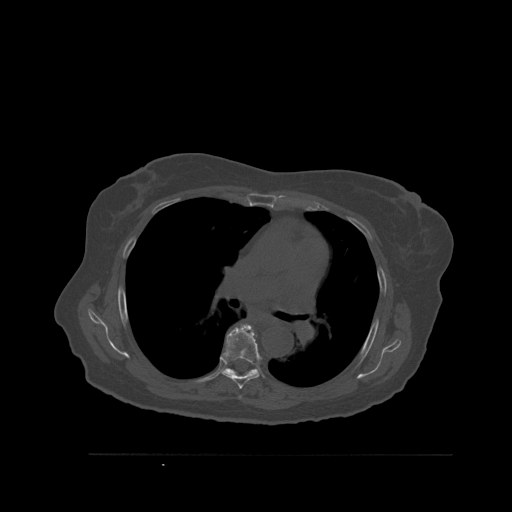
CT including the spine, one axial slice; bone window (W 1800 / L 400 HU); 1.5 mm slice thickness; 512 × 512 image matrix, field of view 470 × 470 mm. Female patient, age 73 years. From the clinical record (not read from this slice): primary cancer: breast; vertebrae with lytic lesions (as recorded): L2.
Annotated regions visible in this slice (semi-automatically segmented with operator editing):
- T5 vertebra: box from (x=239, y=396) to (x=241, y=399) px
- T6 vertebra: (x=222, y=324)–(x=262, y=389)
- T7 vertebra: (x=225, y=367)–(x=258, y=376)